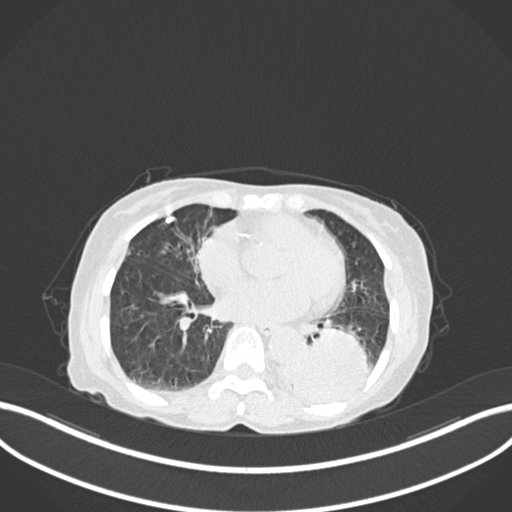
Chest CT, one axial slice; position 55 of 233 along the scan axis; lung window (W 1500 / L -600 HU); 1 mm slice thickness; 512 × 512 image matrix. Patient: female, 78 years. Case-level facts recorded for this patient, not image findings: clinical TNM (as recorded): T3 N0 M1.
Structures marked on this image (rectangle marked by the reading radiologist):
- lung tumour (recorded histology: squamous cell carcinoma): box from (x=279, y=321) to (x=372, y=410) px